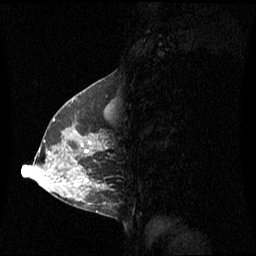
Breast MRI (dynamic contrast-enhanced), one sagittal slice. Slice 25 of 60 in the series (ordered by position). Dynamic contrast-enhanced series, image 2 of 3 at this slice position (ordered by acquisition). 1.5 T. TE 4.2 ms, TR 8.4 ms. 256 × 256 image matrix, field of view 270 × 270 mm. Patient: female, 42 years. Case-level facts recorded for this patient, not image findings: setting: breast cancer imaged before/during neoadjuvant chemotherapy; receptor status: HR-positive, HER2-negative.
Structures marked on this image (semi-automatically segmented with operator editing):
- analysis volume of interest (the breast-tissue region the enhancement analysis was run in; not a lesion): bounding box [x1, y1, x2, y2] px = [56, 104, 111, 185]
- tumour enhancement mask (voxels above the 70 % enhancement threshold inside the analysis volume of interest): [81, 145, 87, 181]